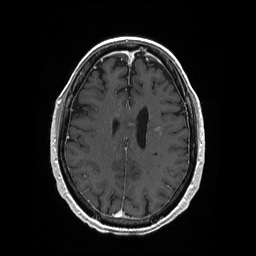
Brain MRI from a brain-tumour surgery series, one axial slice; T1-weighted post-contrast; 256 × 256 image matrix, field of view 256 × 256 mm. Case-level facts recorded for this patient, not image findings: histopathology: Primary diffuse large B-cell lymphoma.
Structures marked on this image (manually delineated by an expert):
- tumour: bounding box (x1, y1, x2, y2) in pixels: (129, 123, 162, 132)